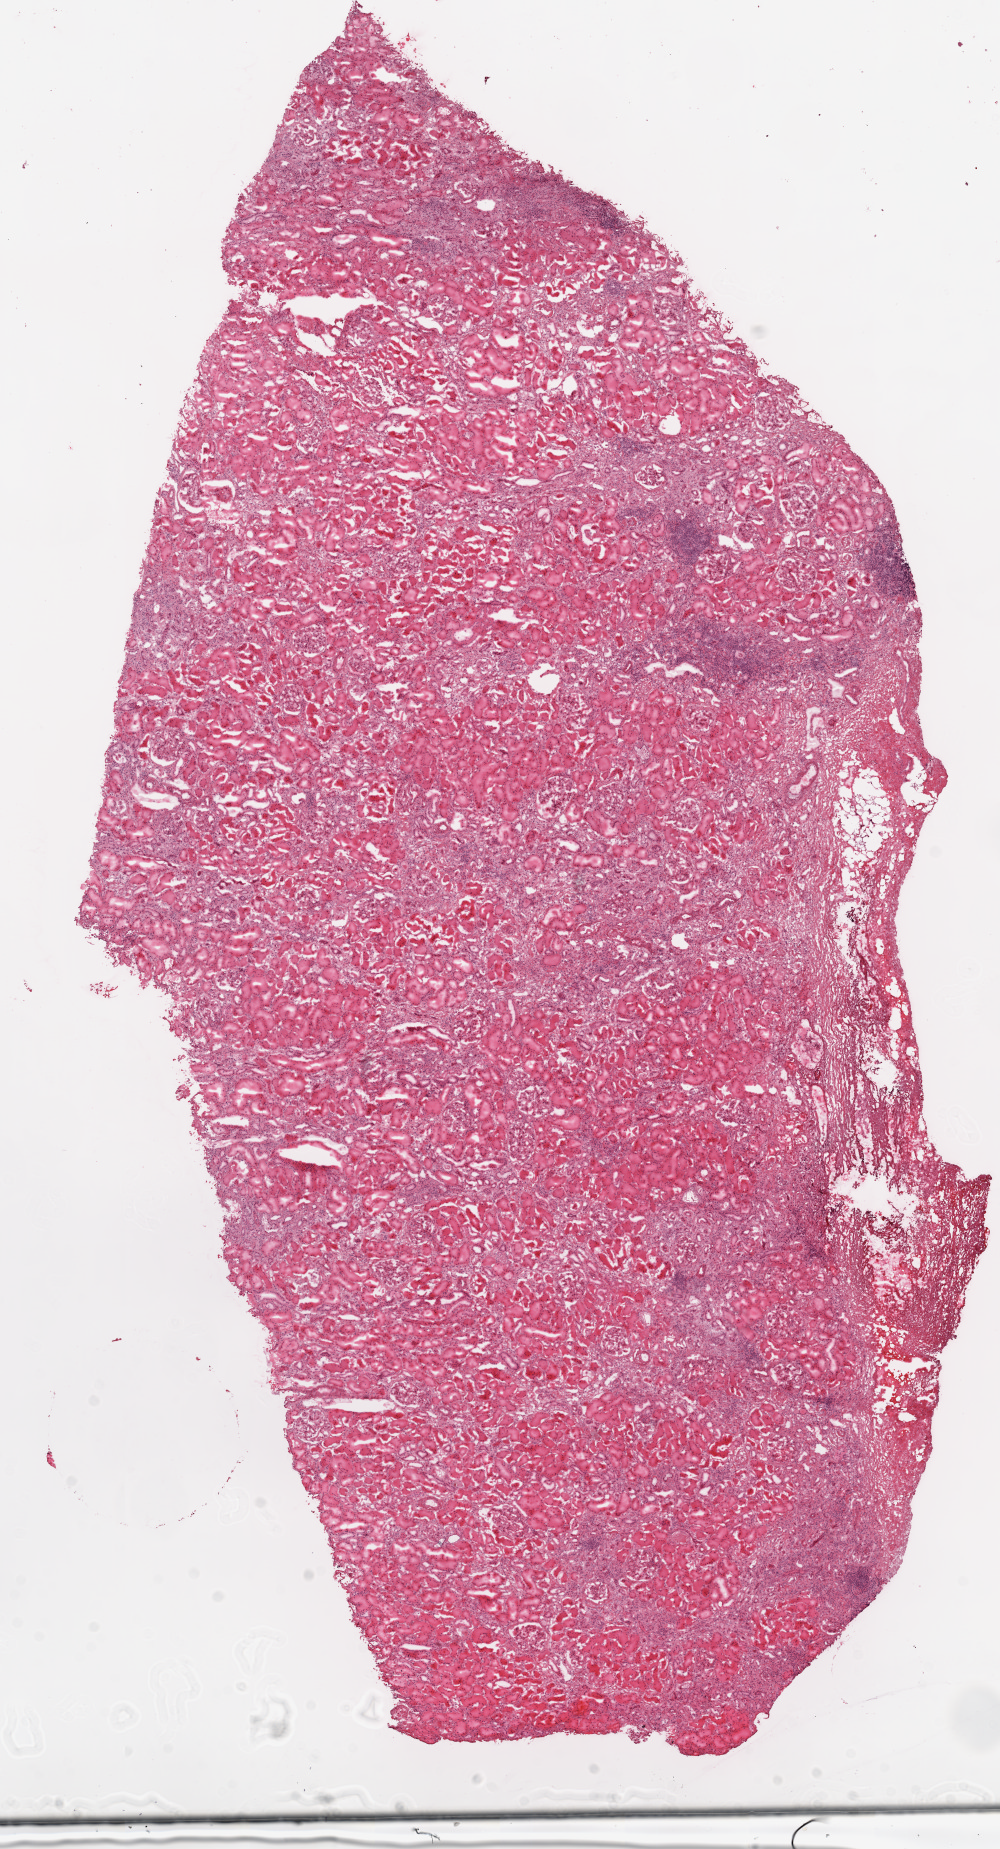
Whole-slide histology image, H&E, shown as a low-resolution overview of the whole scanned area (about 8.0 x 14.8 mm, acquisition: 20x scan), frozen section from the top of the tissue portion, solid tissue normal (non-tumour tissue) sample from the kidney. Male patient; age at initial diagnosis 79 years.
This section: solid tissue normal sample (biorepository sample class). Patient diagnosis: Clear cell adenocarcinoma, NOS.